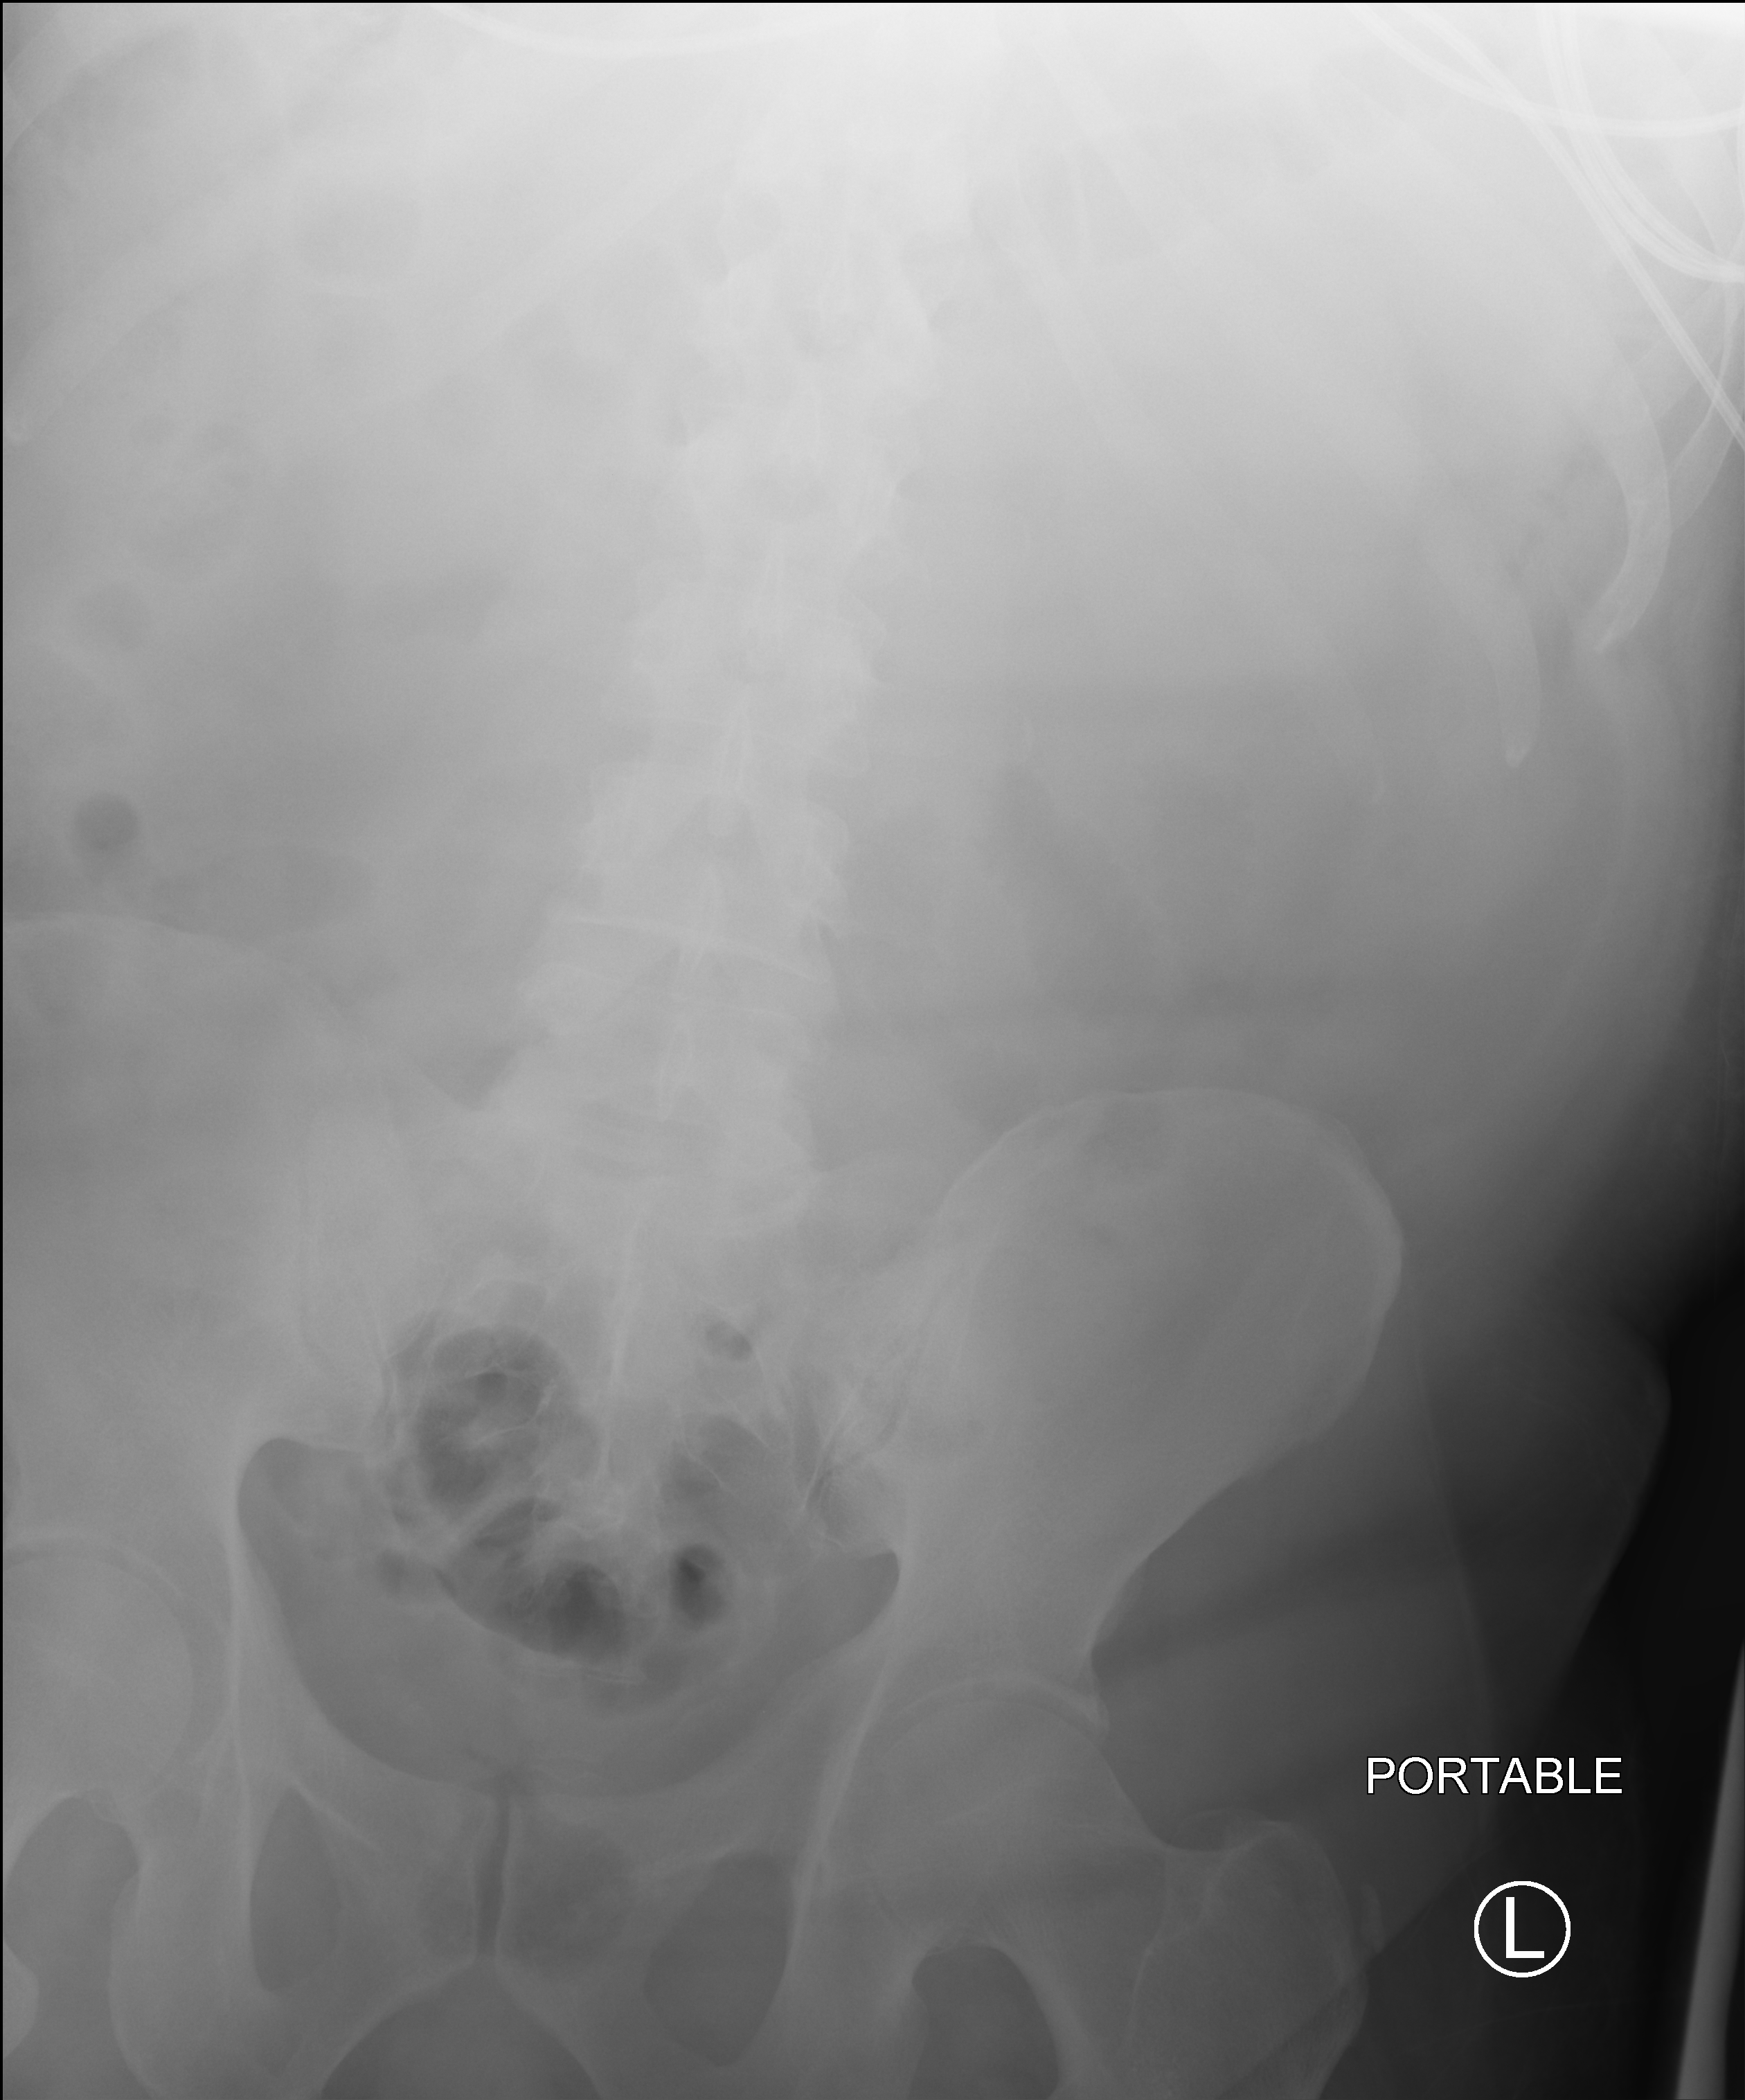
Bedside abdomen radiograph (computed radiography). Patient hospitalised with COVID-19; male, aged 18–59 years.
Hospital-stay facts (about this admission, not read from this image; timing relative to this image not recorded): chronic kidney disease (admission record): no.